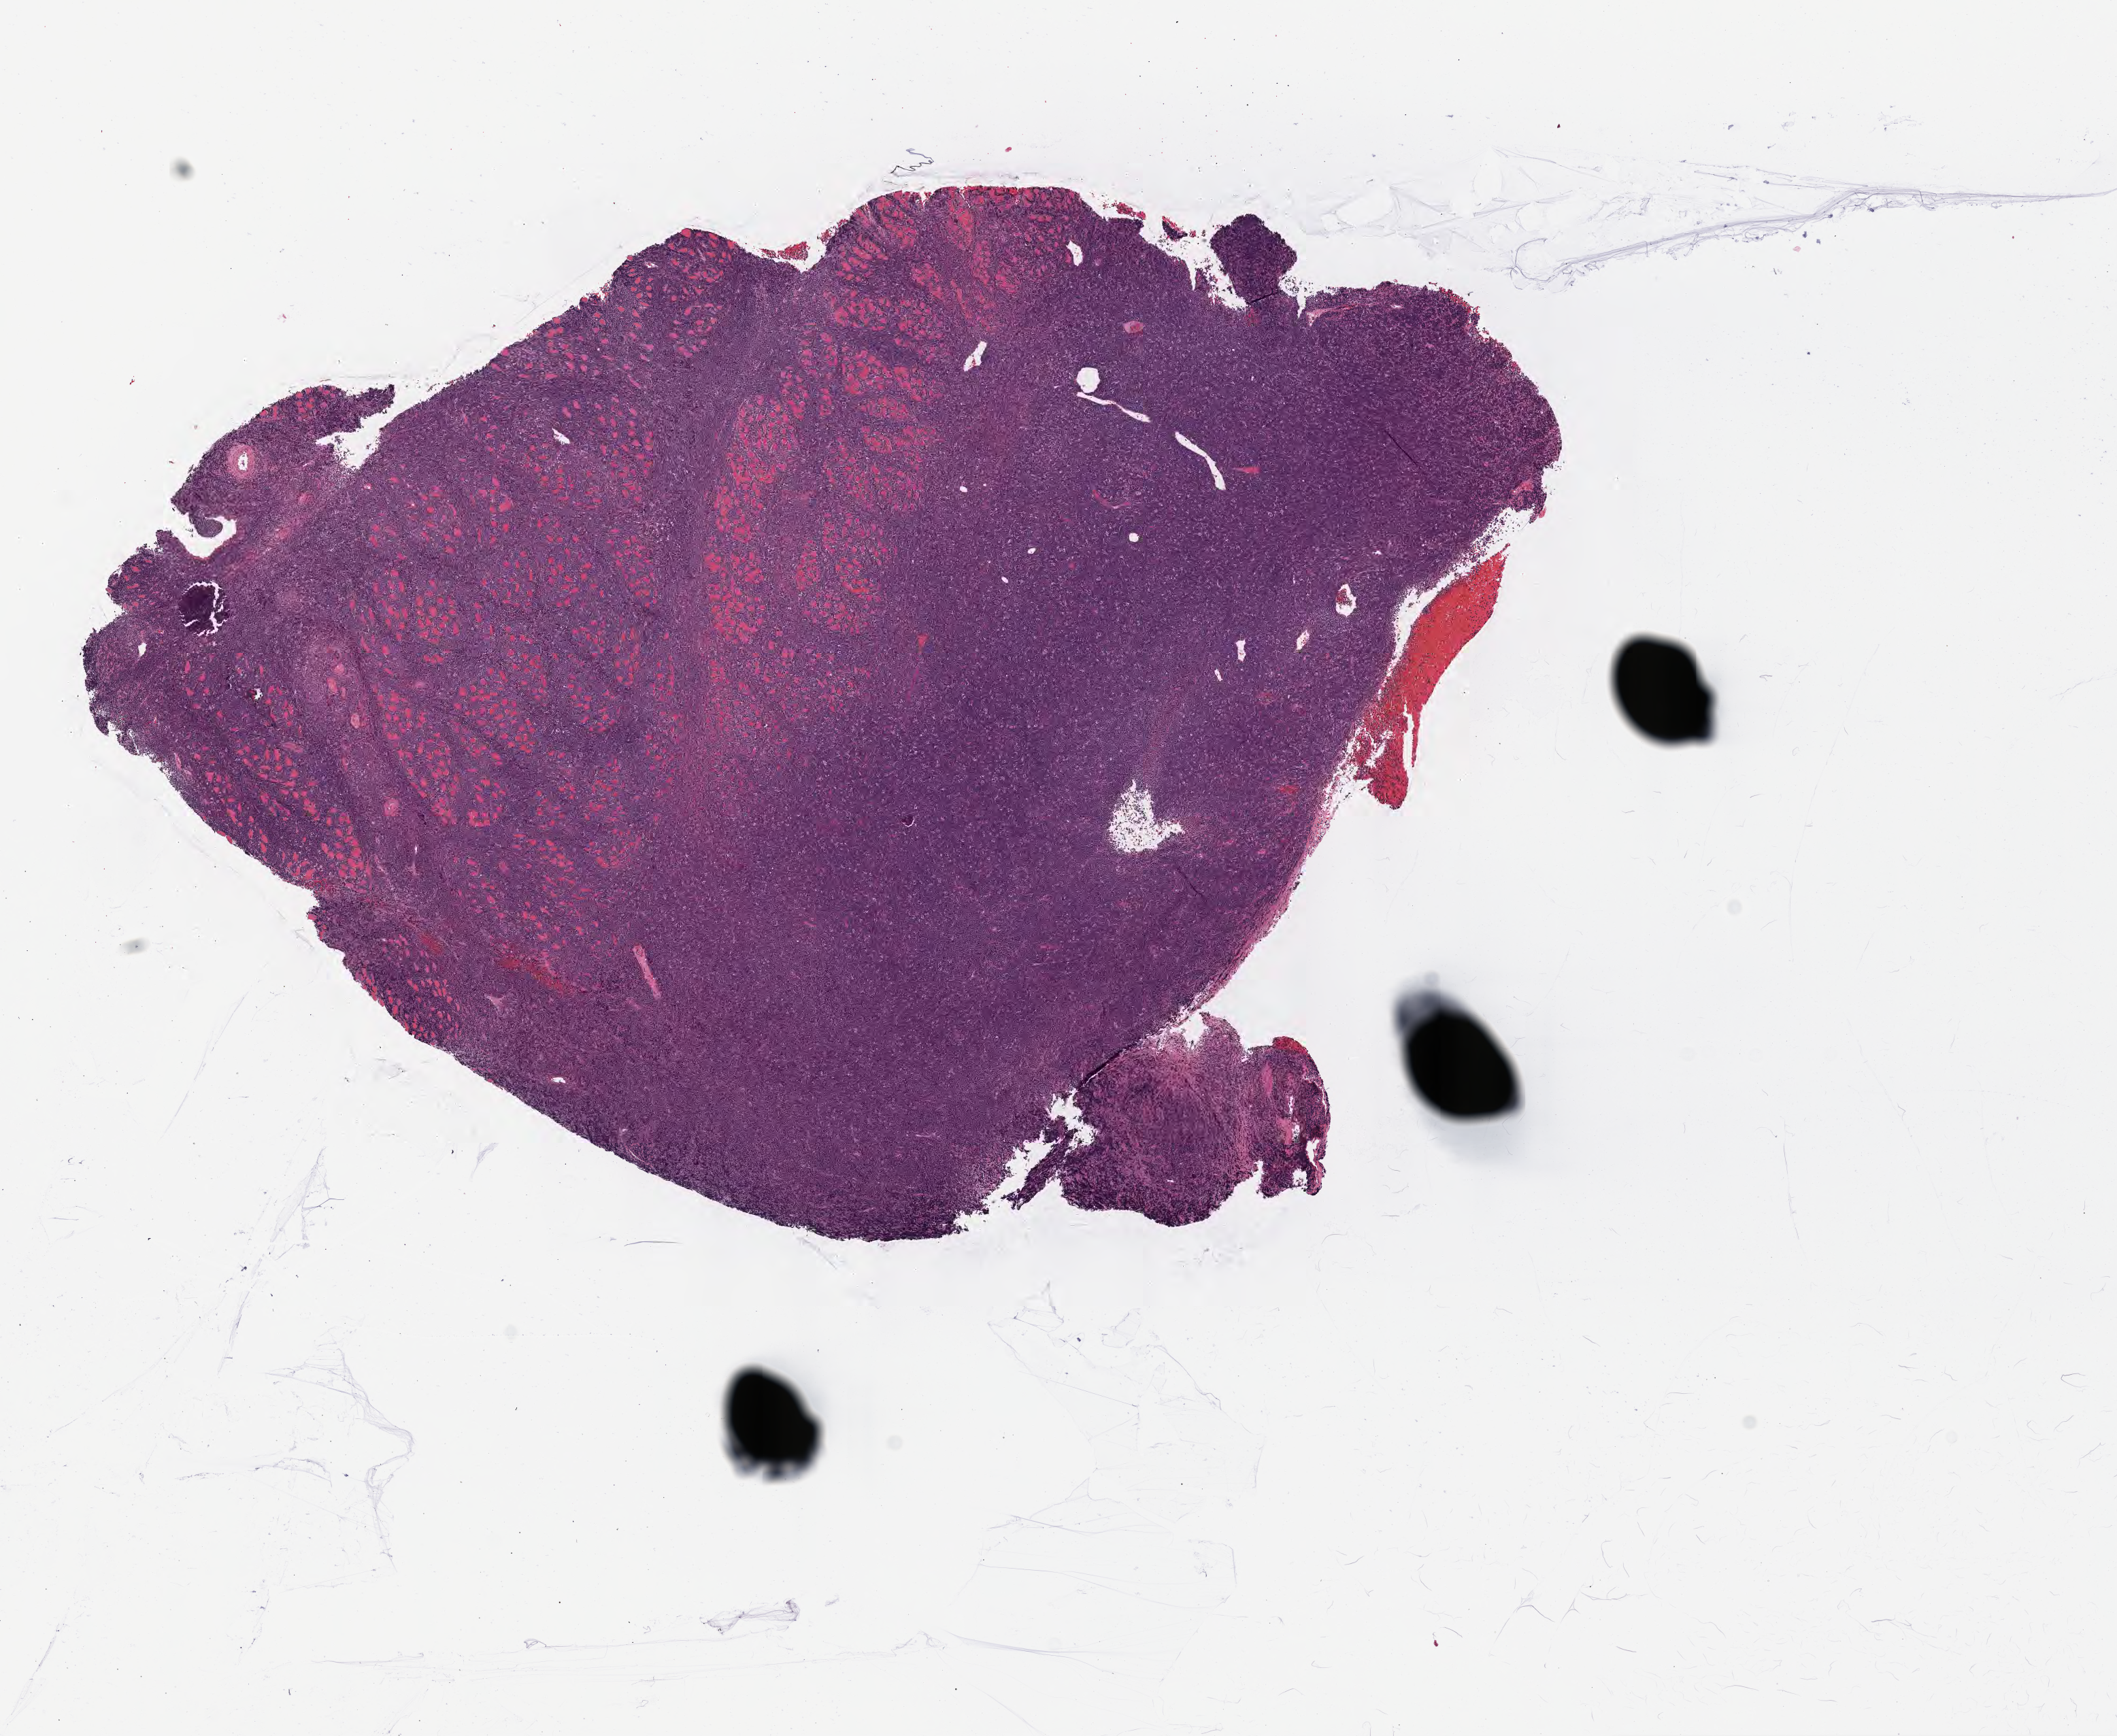
Haematoxylin and eosin whole-slide image — a low-resolution overview of the entire scanned area, about 12.6 x 10.3 mm. Specimen: tumor tissue. Site: cranium. Male patient, aged 46.
• histologic diagnosis: Burkitt lymphoma, NOS